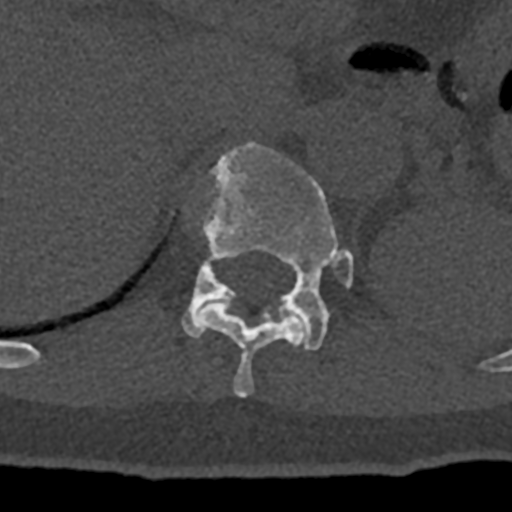
CT including the spine, one axial slice; slice 518 of 797 in the series (ordered by position); reconstruction kernel Br40s/3; 120 kVp; bone window (W 1800 / L 400 HU); 512 × 512 image matrix. Patient: male, 74 years. From the clinical record (not read from this slice): primary cancer: renal; vertebrae with lytic lesions (as recorded): T10, L1, L2, L3, L4, L5.
Annotated regions visible in this slice (semi-automatic segmentation, software-assisted and operator-edited):
- T11 vertebra: bounding box [x1, y1, x2, y2] px = [194, 302, 306, 397]
- T12 vertebra: [182, 142, 353, 350]